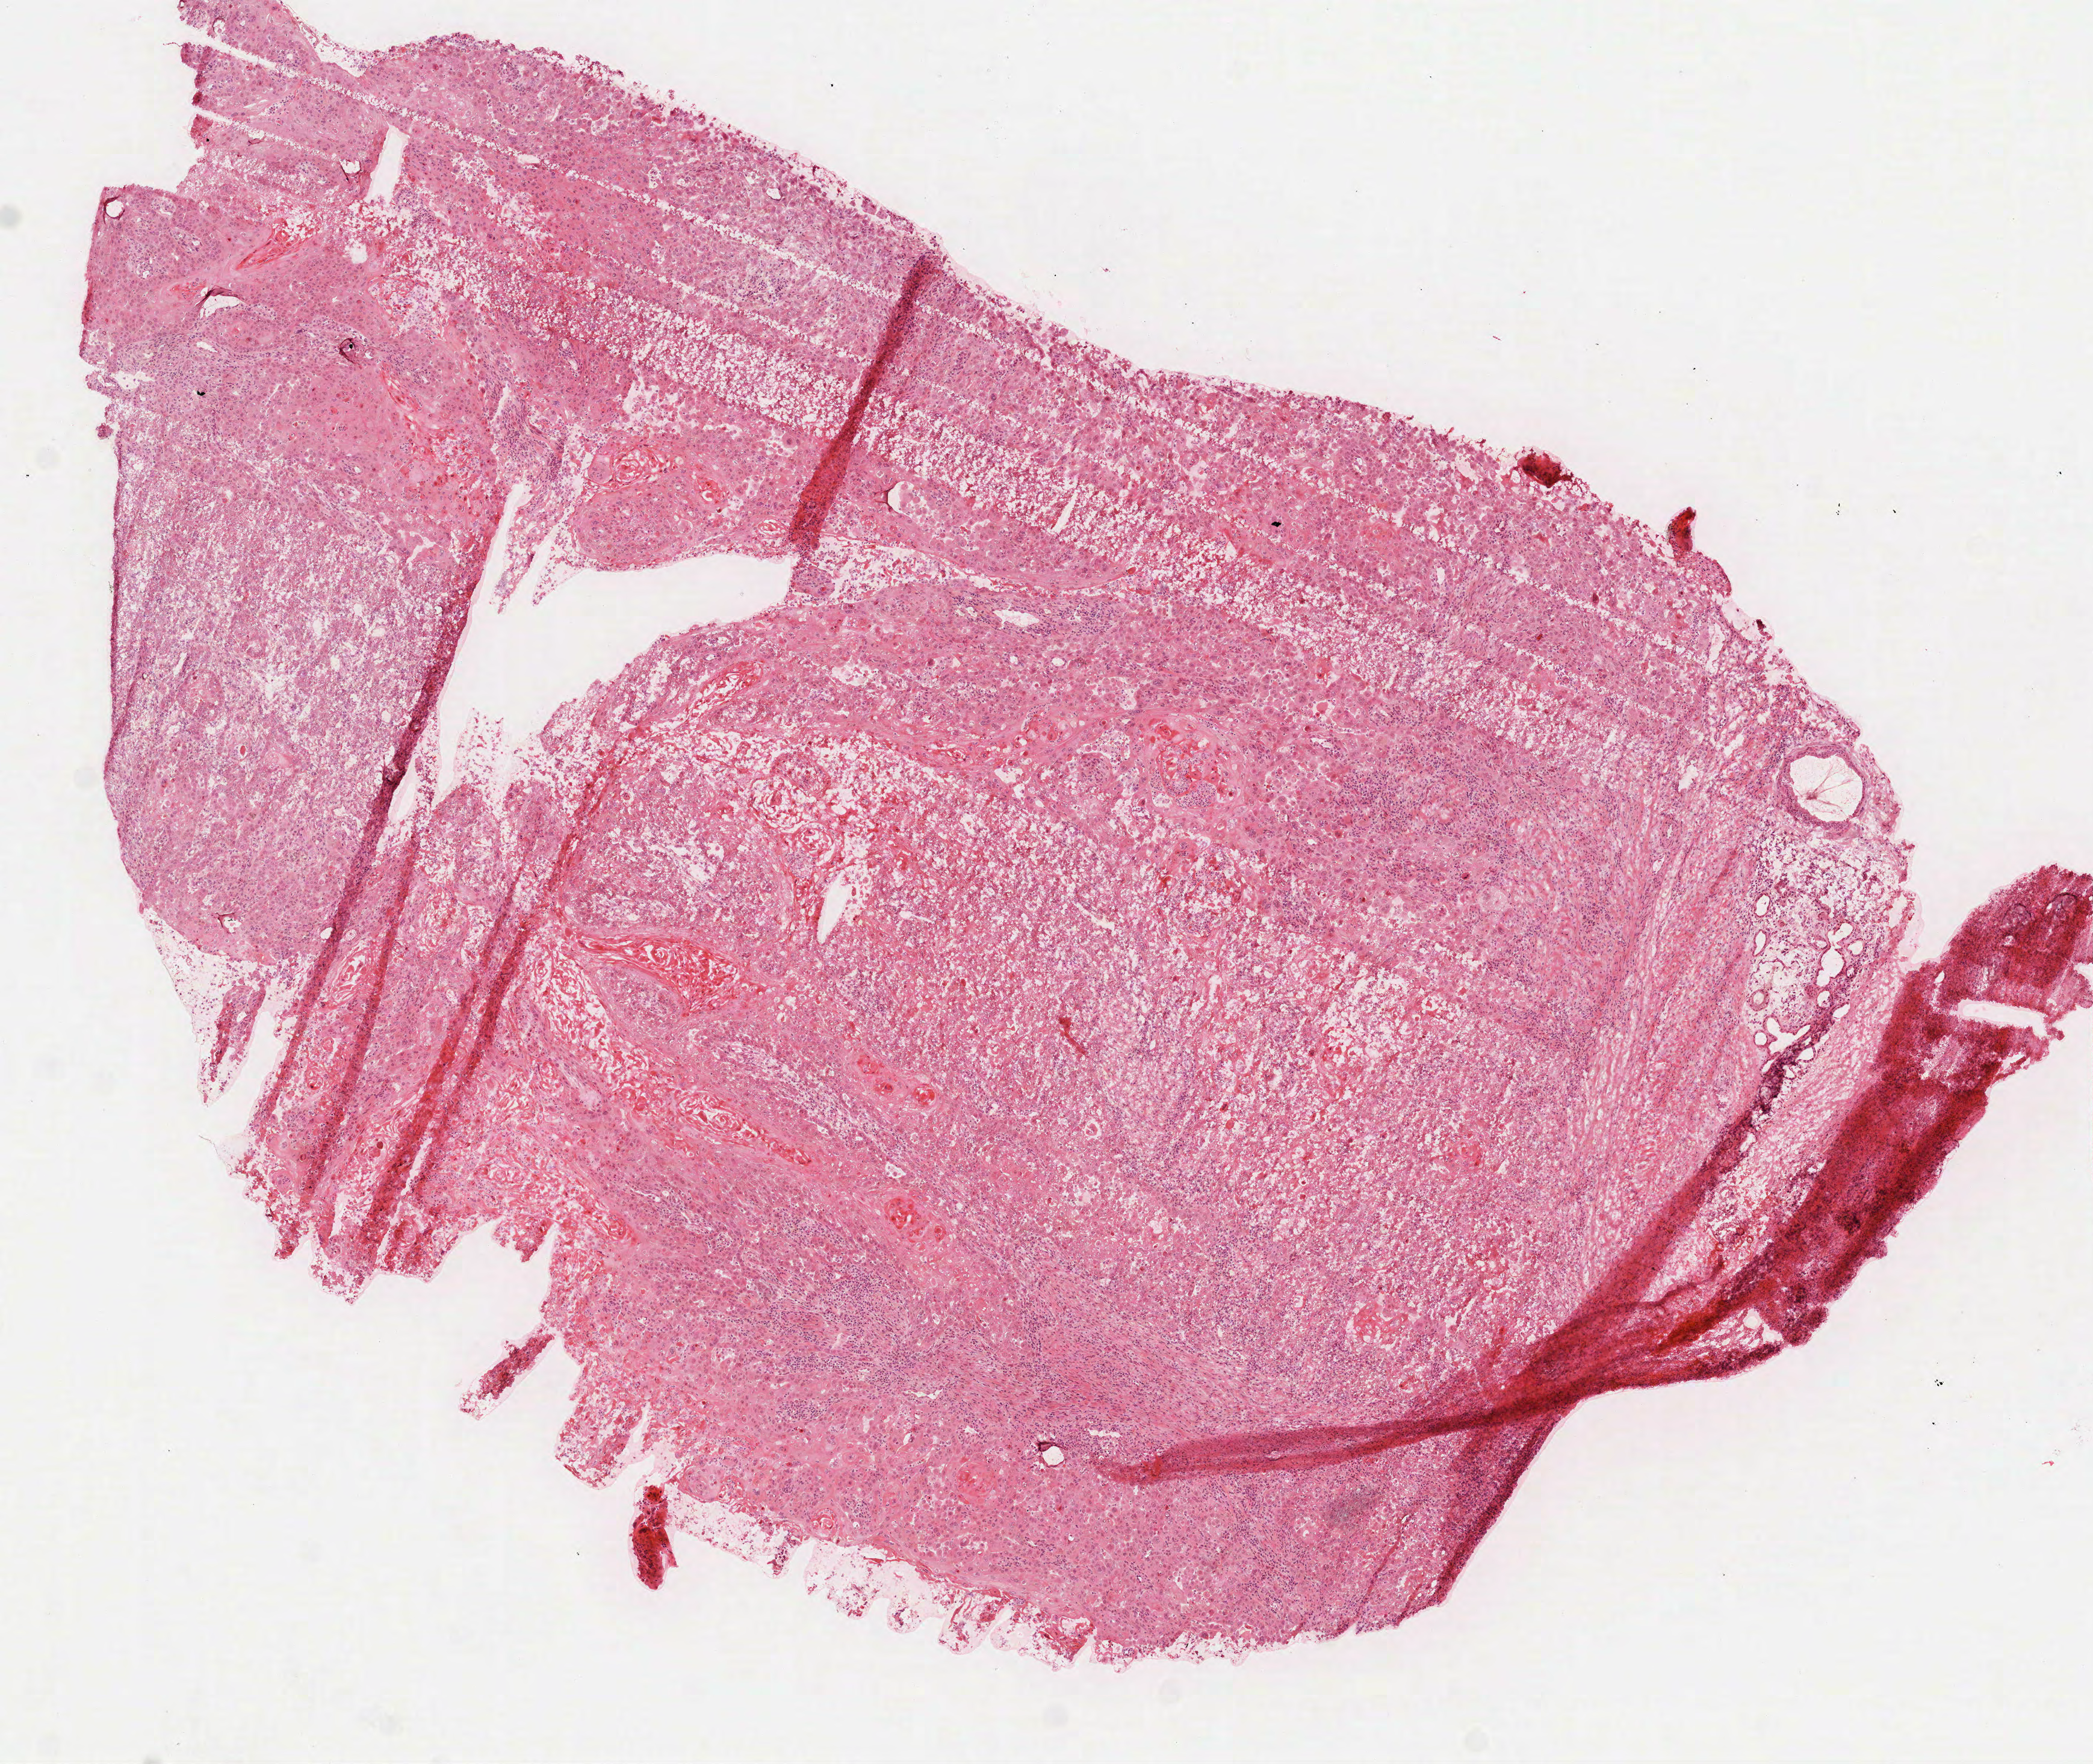
Whole-slide histology image, H&E — whole scanned area (about 7.0 x 5.9 mm, from a 40x scan) shown as a low-resolution overview. Frozen section from the top of the tissue portion. Primary tumour sample from the head and neck. Patient: male, age at initial diagnosis 61 years. Slide review estimates, as recorded: tumour cells 90%, tumour nuclei 70%.
Pathologic diagnosis: Squamous cell carcinoma, NOS (larynx, NOS).